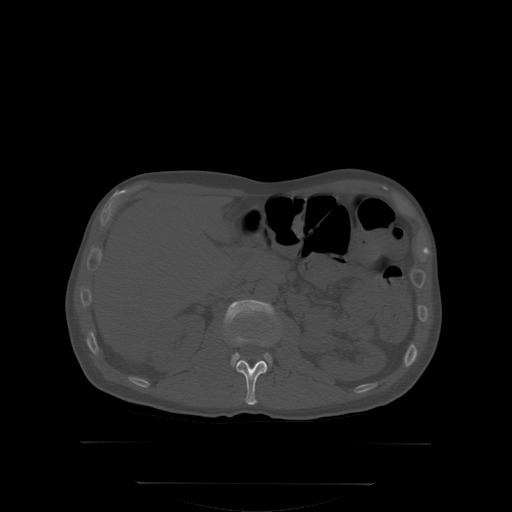
CT including the spine, one axial slice. Position 147 of 350 along the scan axis. Bone window (W 1800 / L 400 HU). 512 × 512 image matrix. Male patient, age 58 years. From the clinical record (not read from this slice): primary cancer: prostate; vertebrae with lytic lesions (as recorded): L1.
Structures marked on this image (semi-automatic segmentation, software-assisted and operator-edited):
- L1 vertebra: box from (x=227, y=335) to (x=278, y=405) px
- L2 vertebra: (x=226, y=301)–(x=279, y=368)